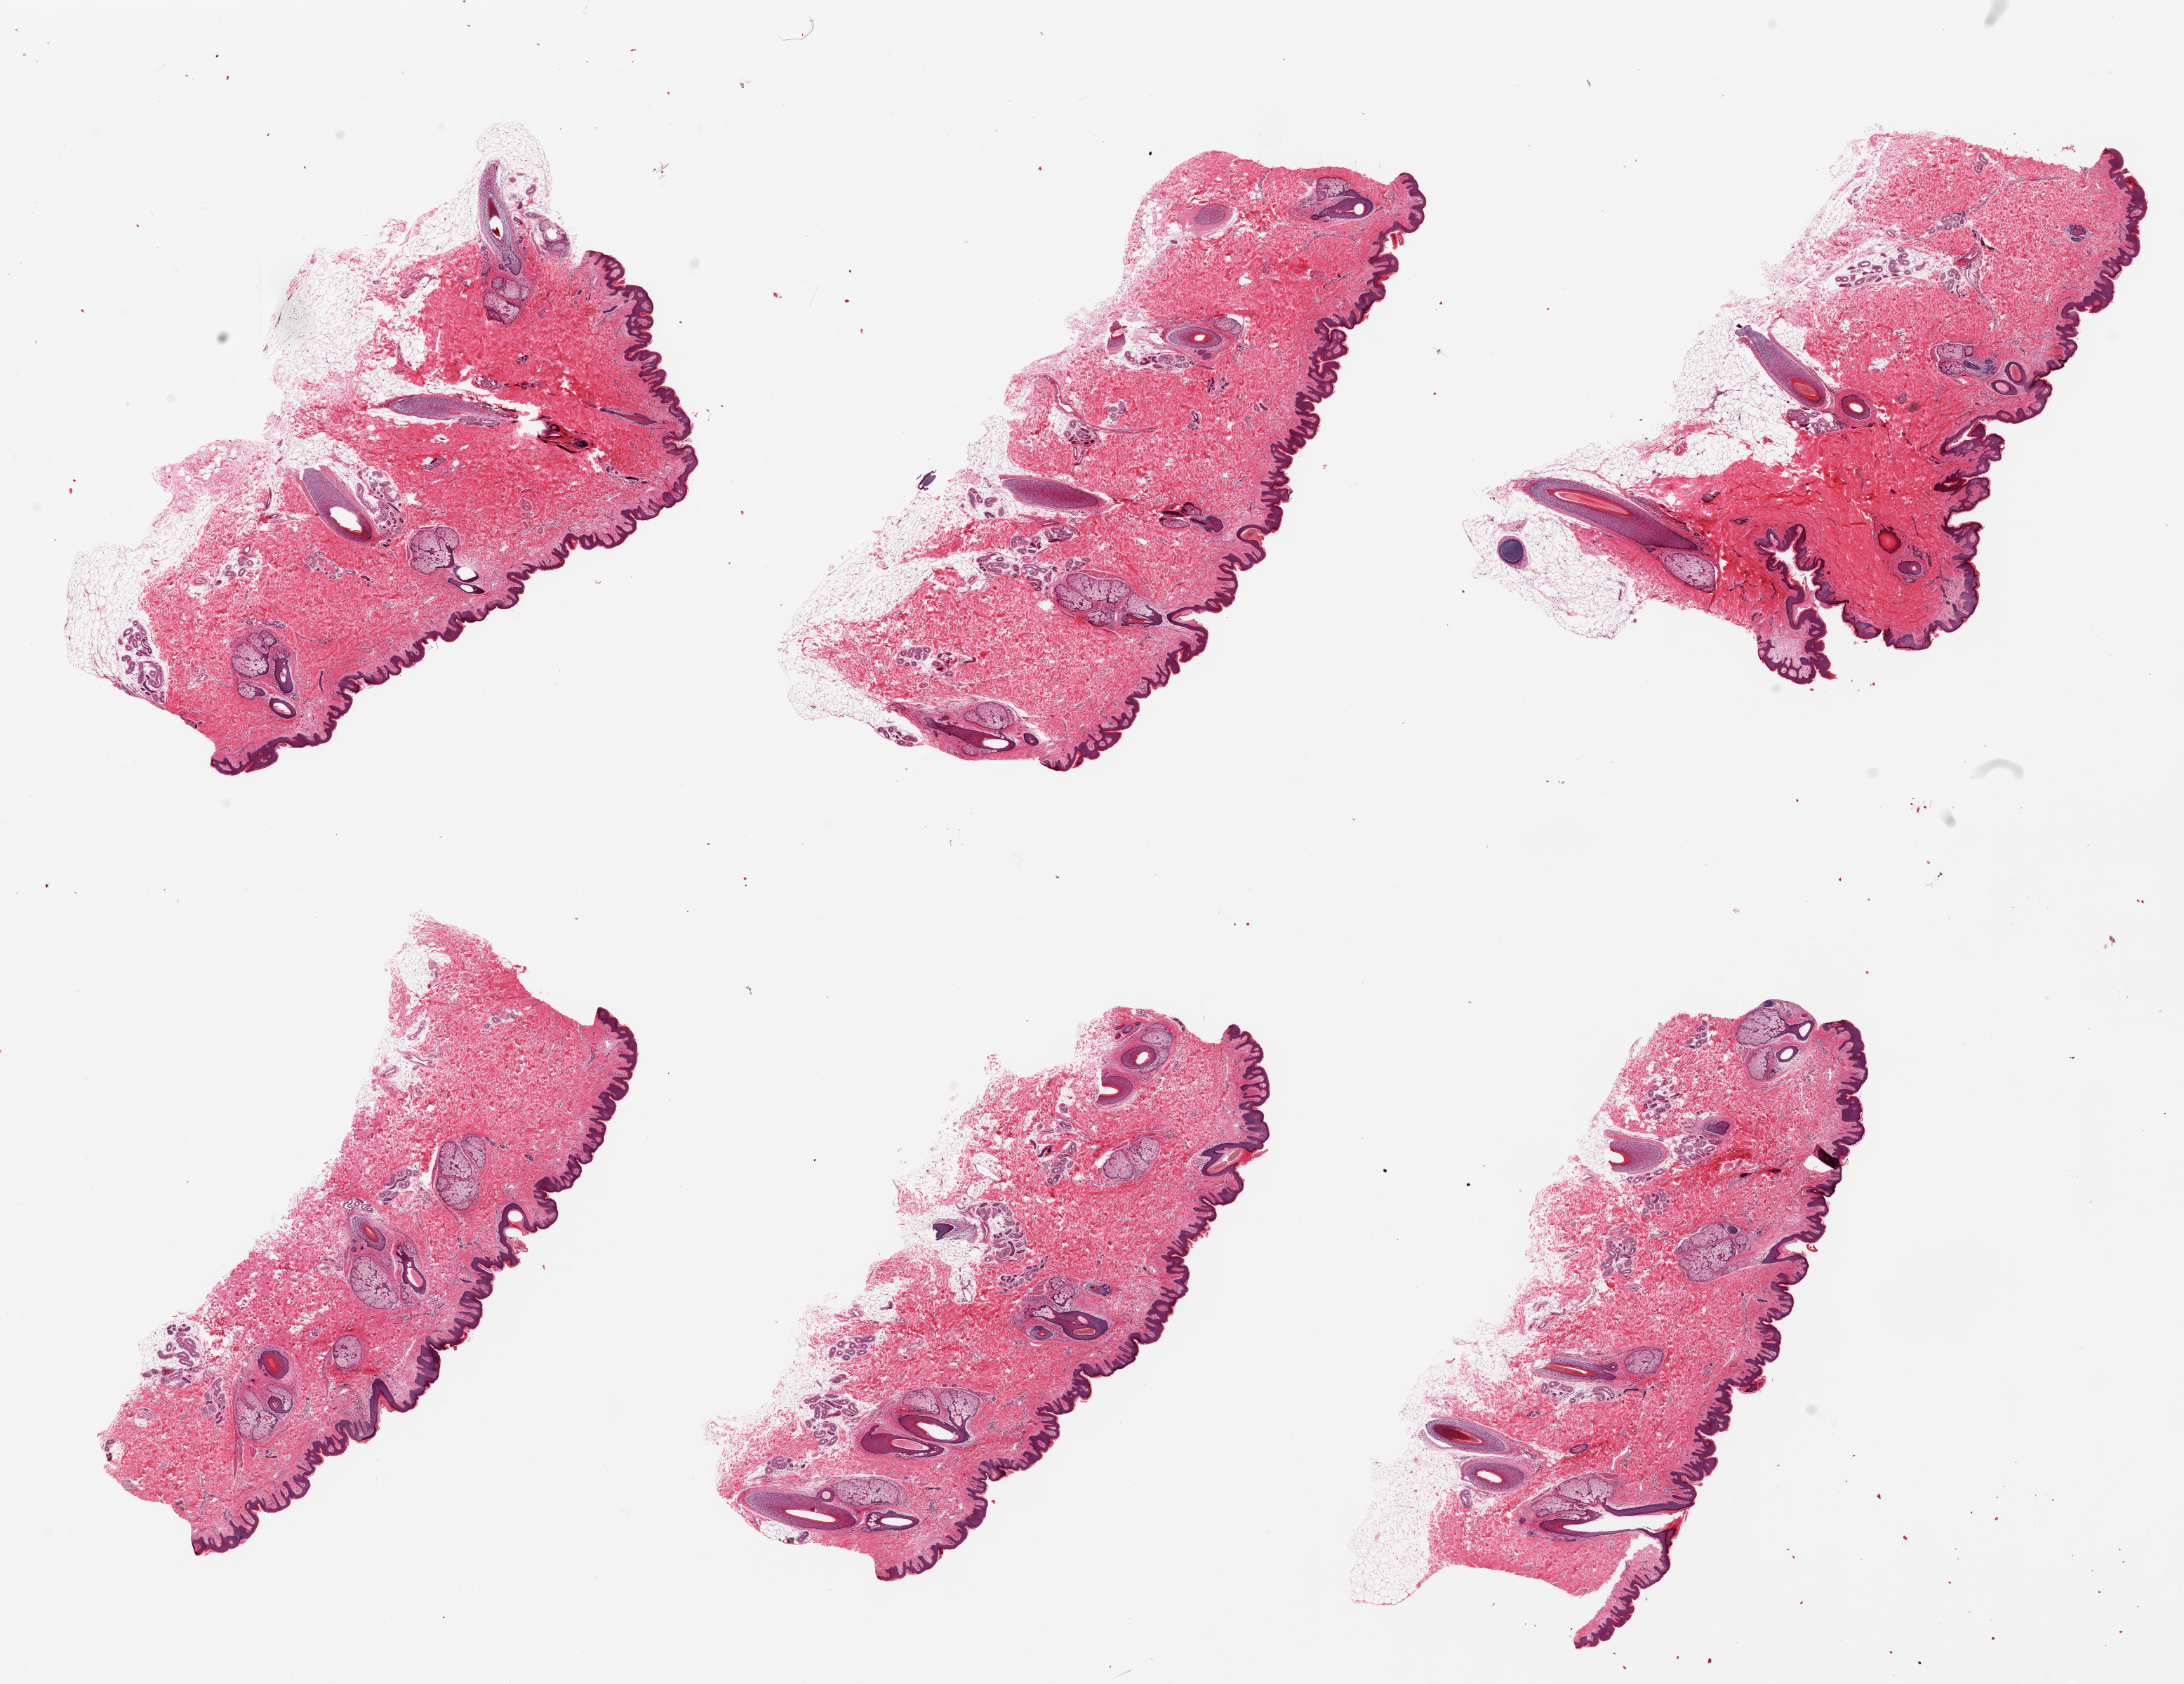
Whole-slide image, H&E stain, brightfield — shown as a low-resolution overview of the whole scanned area (about 24.6 x 19.0 mm, slide scanned at 20x). PAXgene-fixed, paraffin-embedded tissue. Section of skin of suprapubic region (target tissue). Tissue donor sample. Donor sex: male.
Pathologist's review note for this sample: 6 pieces; numerous hair follicles.